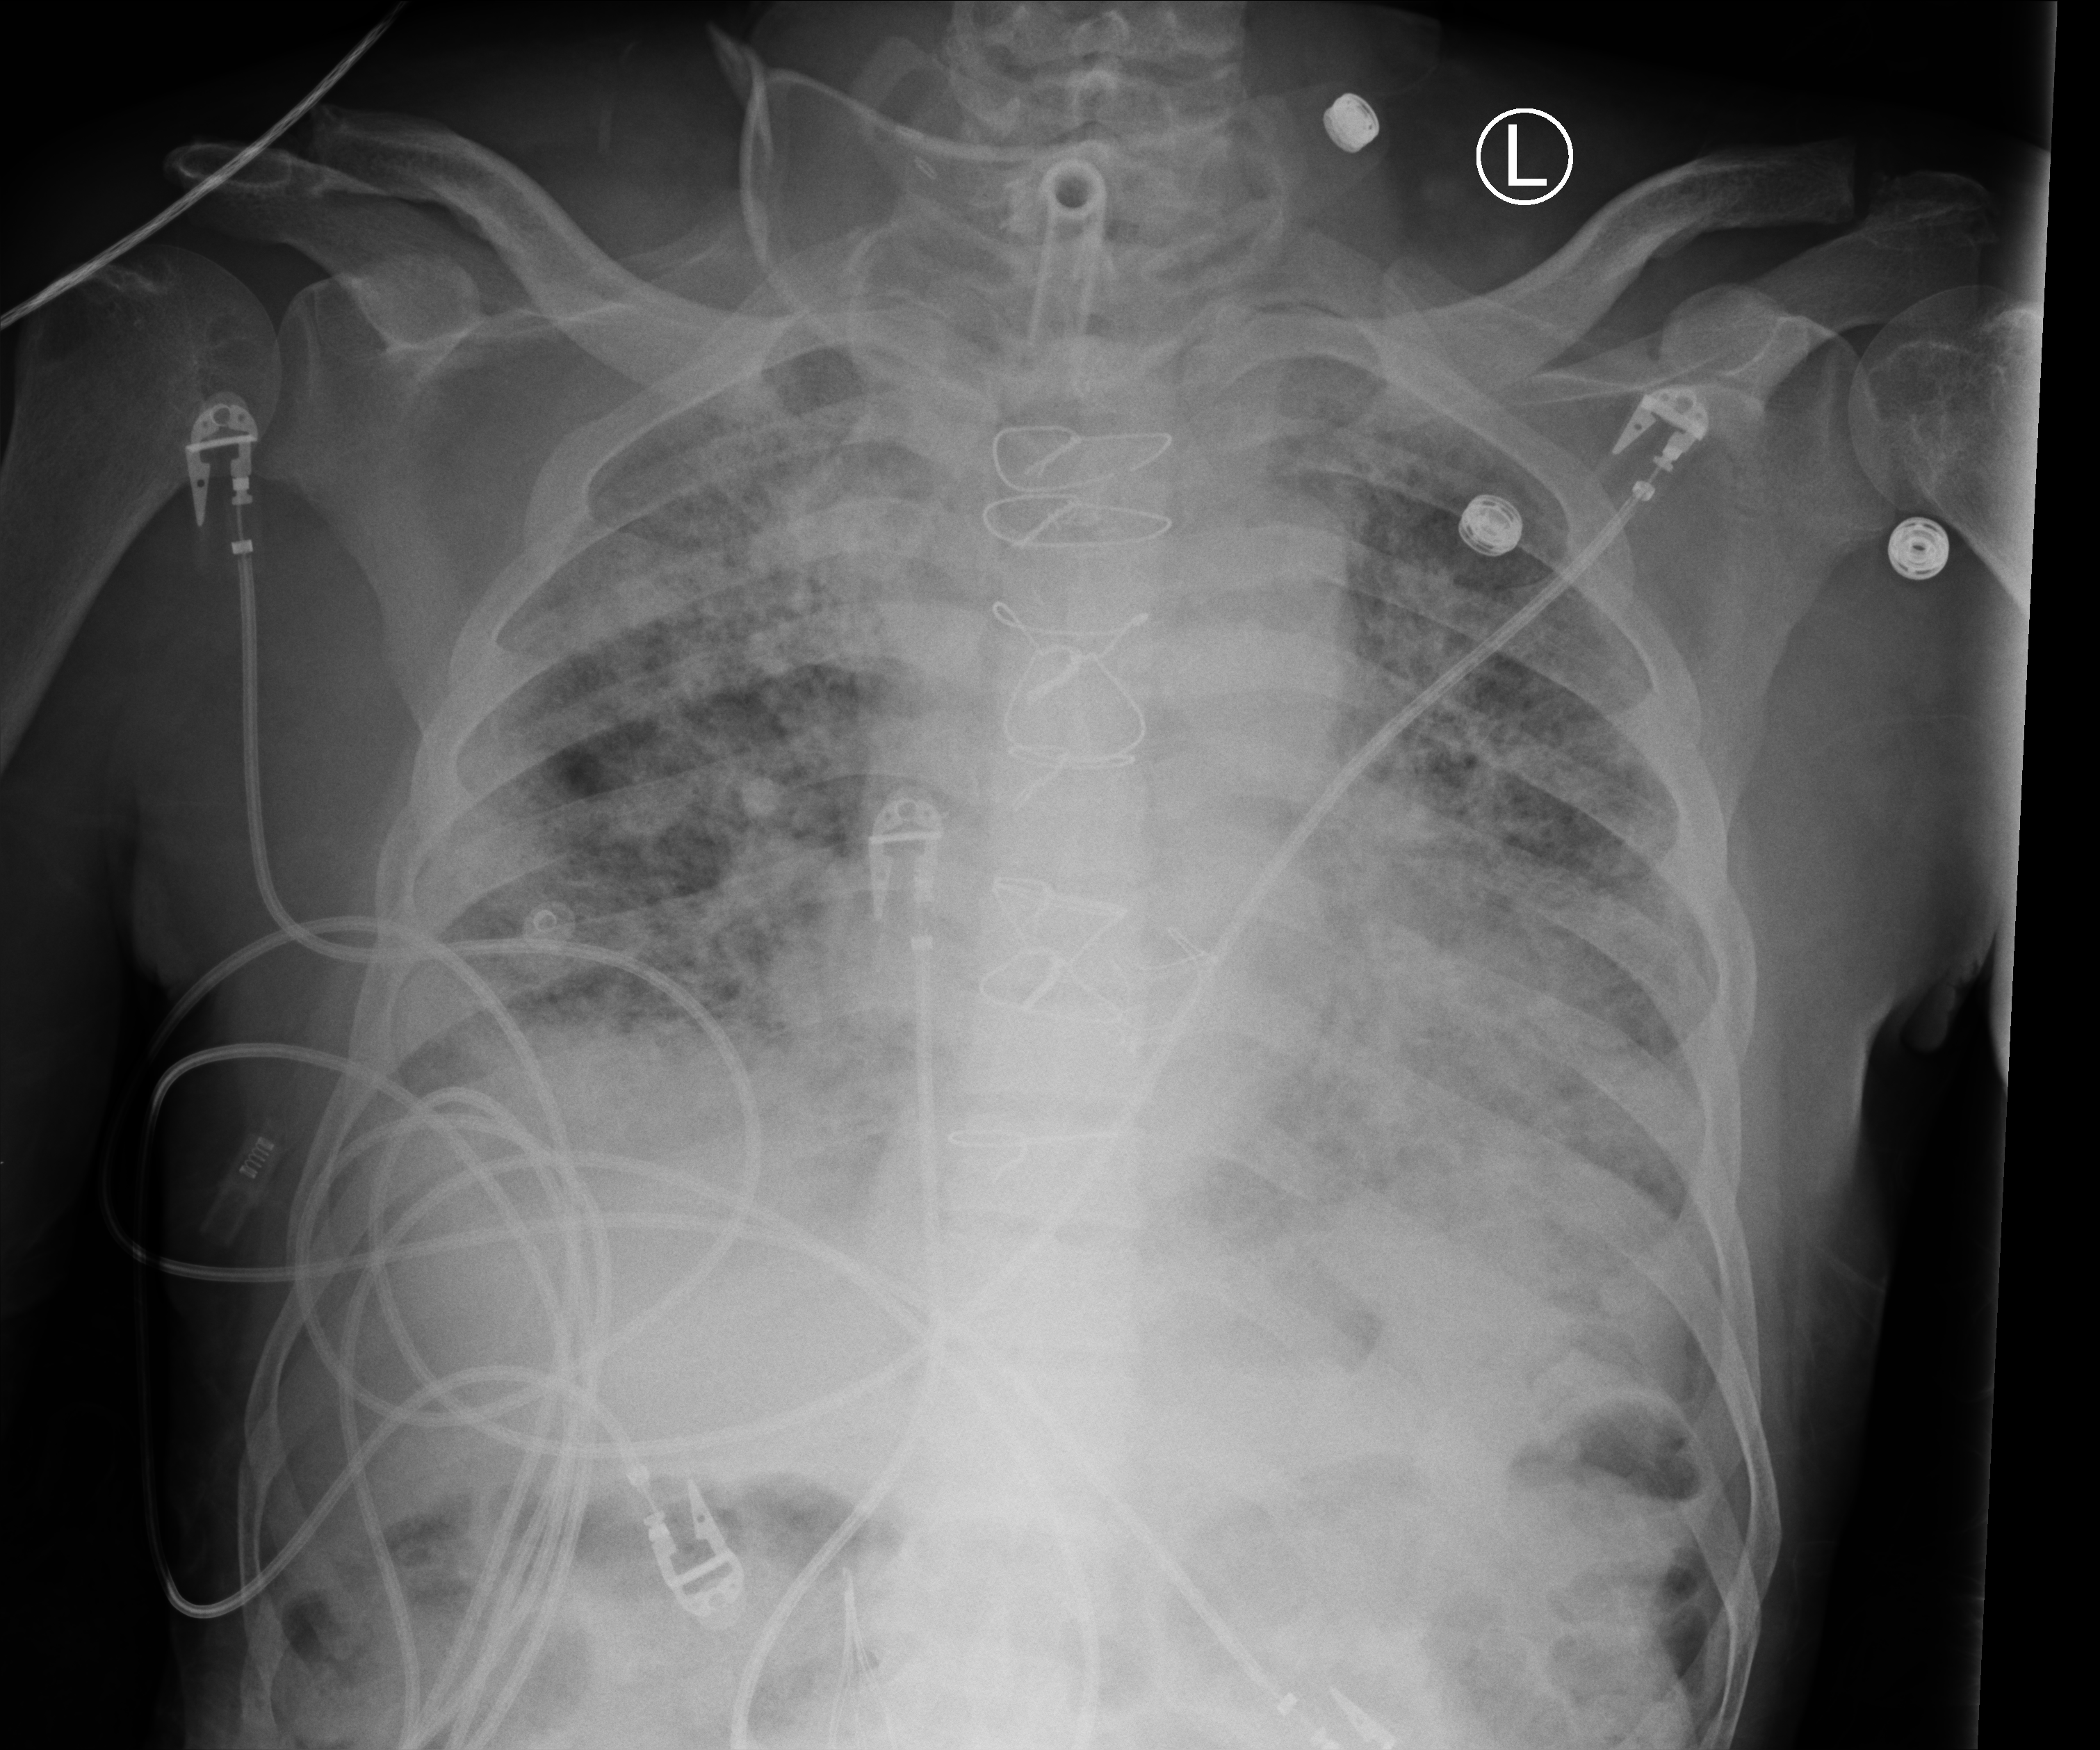
Chest X-ray (portable), anteroposterior (AP) projection. Patient hospitalised with COVID-19; male, aged 60–74 years.
Hospital-stay facts (about this admission, not read from this image; timing relative to this image not recorded):
- chronic kidney disease (admission record): no
- length of hospital stay: 50 days
- hypertension (admission record): no